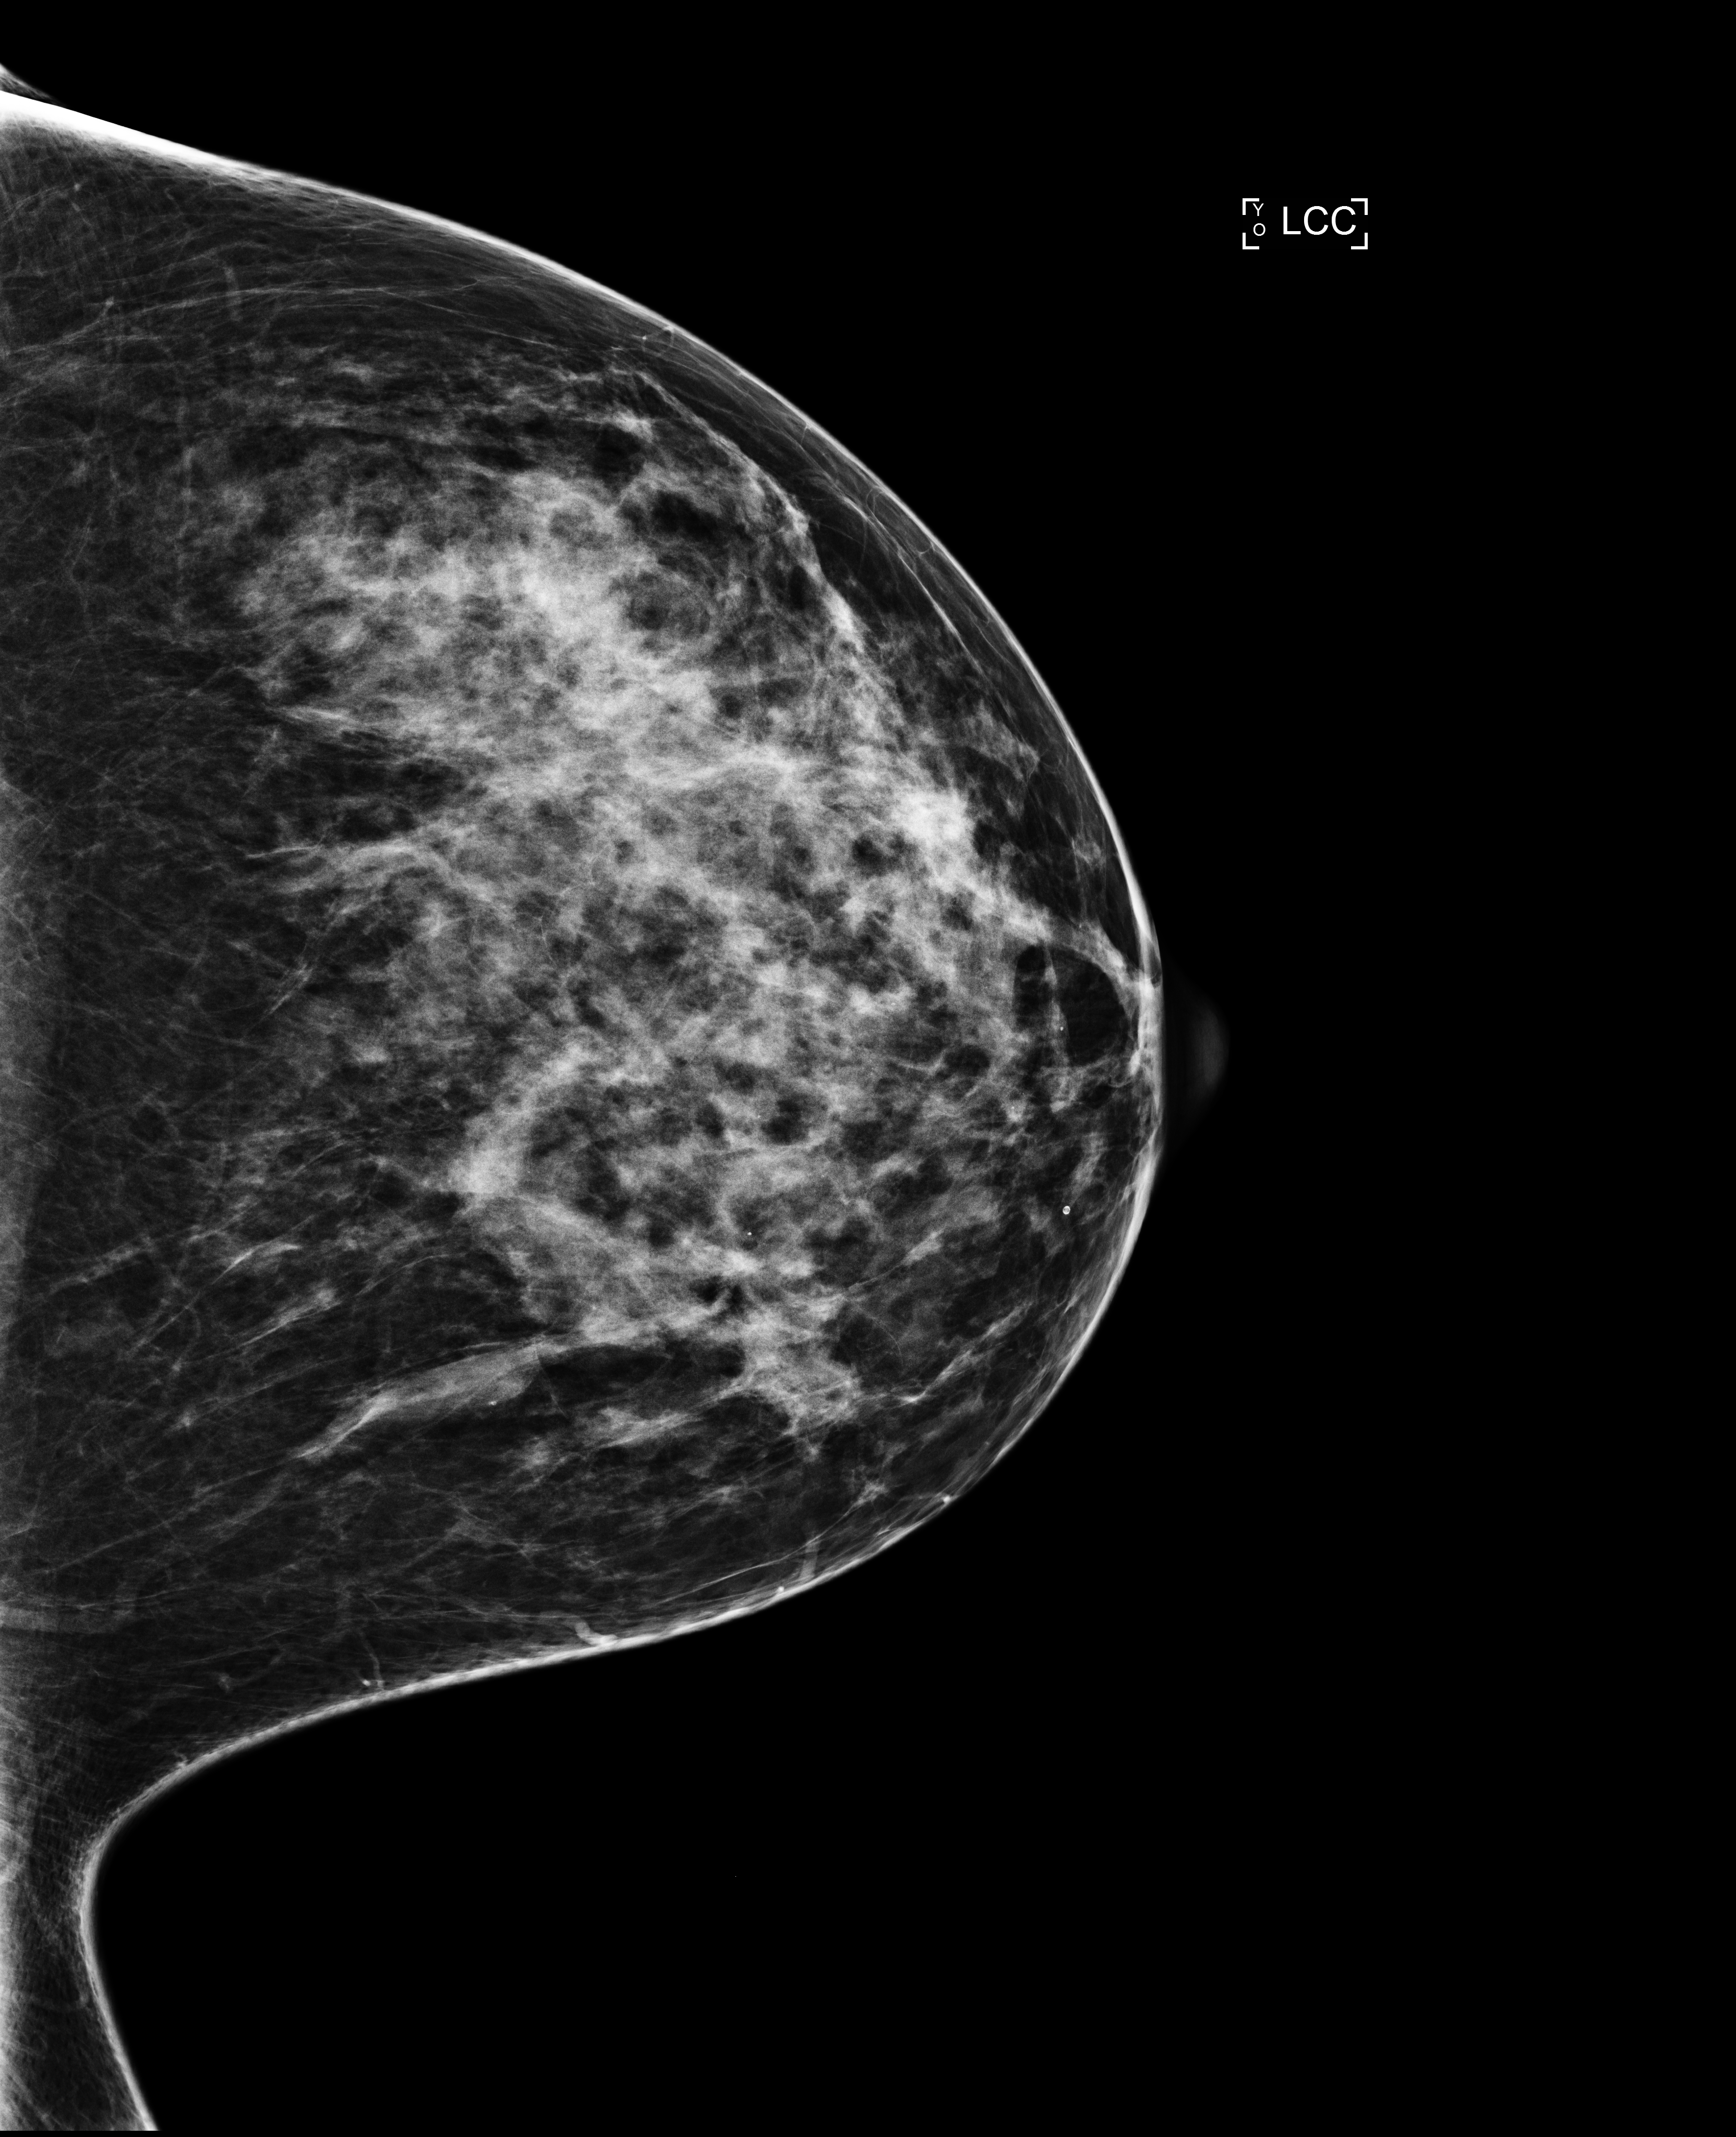
Annual screening mammography examination, compressed breast thickness 64 mm. Female patient, age 46 years.
Image type: full-field digital mammogram. Breast: left. Projection: CC view.